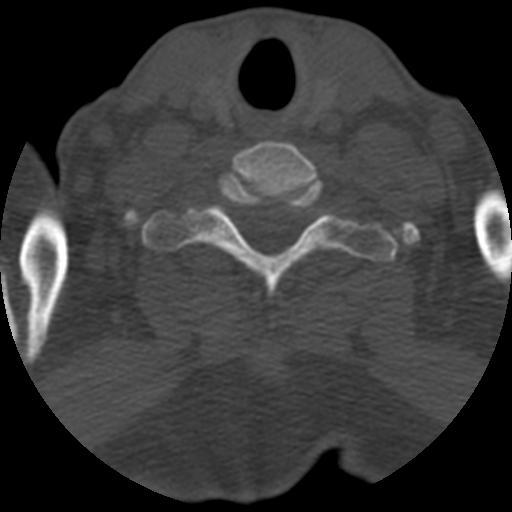
CT including the spine, one axial slice; position 523 of 708 along the scan axis; one of 3 acquisitions stored at this slice position; bone window (W 1800 / L 400 HU); 1.25 mm slice thickness; 512 × 512 image matrix, field of view 160 × 160 mm. Patient age 55 years. Case-level facts recorded for this patient, not image findings: primary cancer: colon; vertebrae with lytic lesions (as recorded): T12, L1, L5.
Structures marked on this image (semi-automatically segmented with operator editing):
- T1 vertebra: bounding box (x1, y1, x2, y2) in pixels: (142, 177, 395, 303)